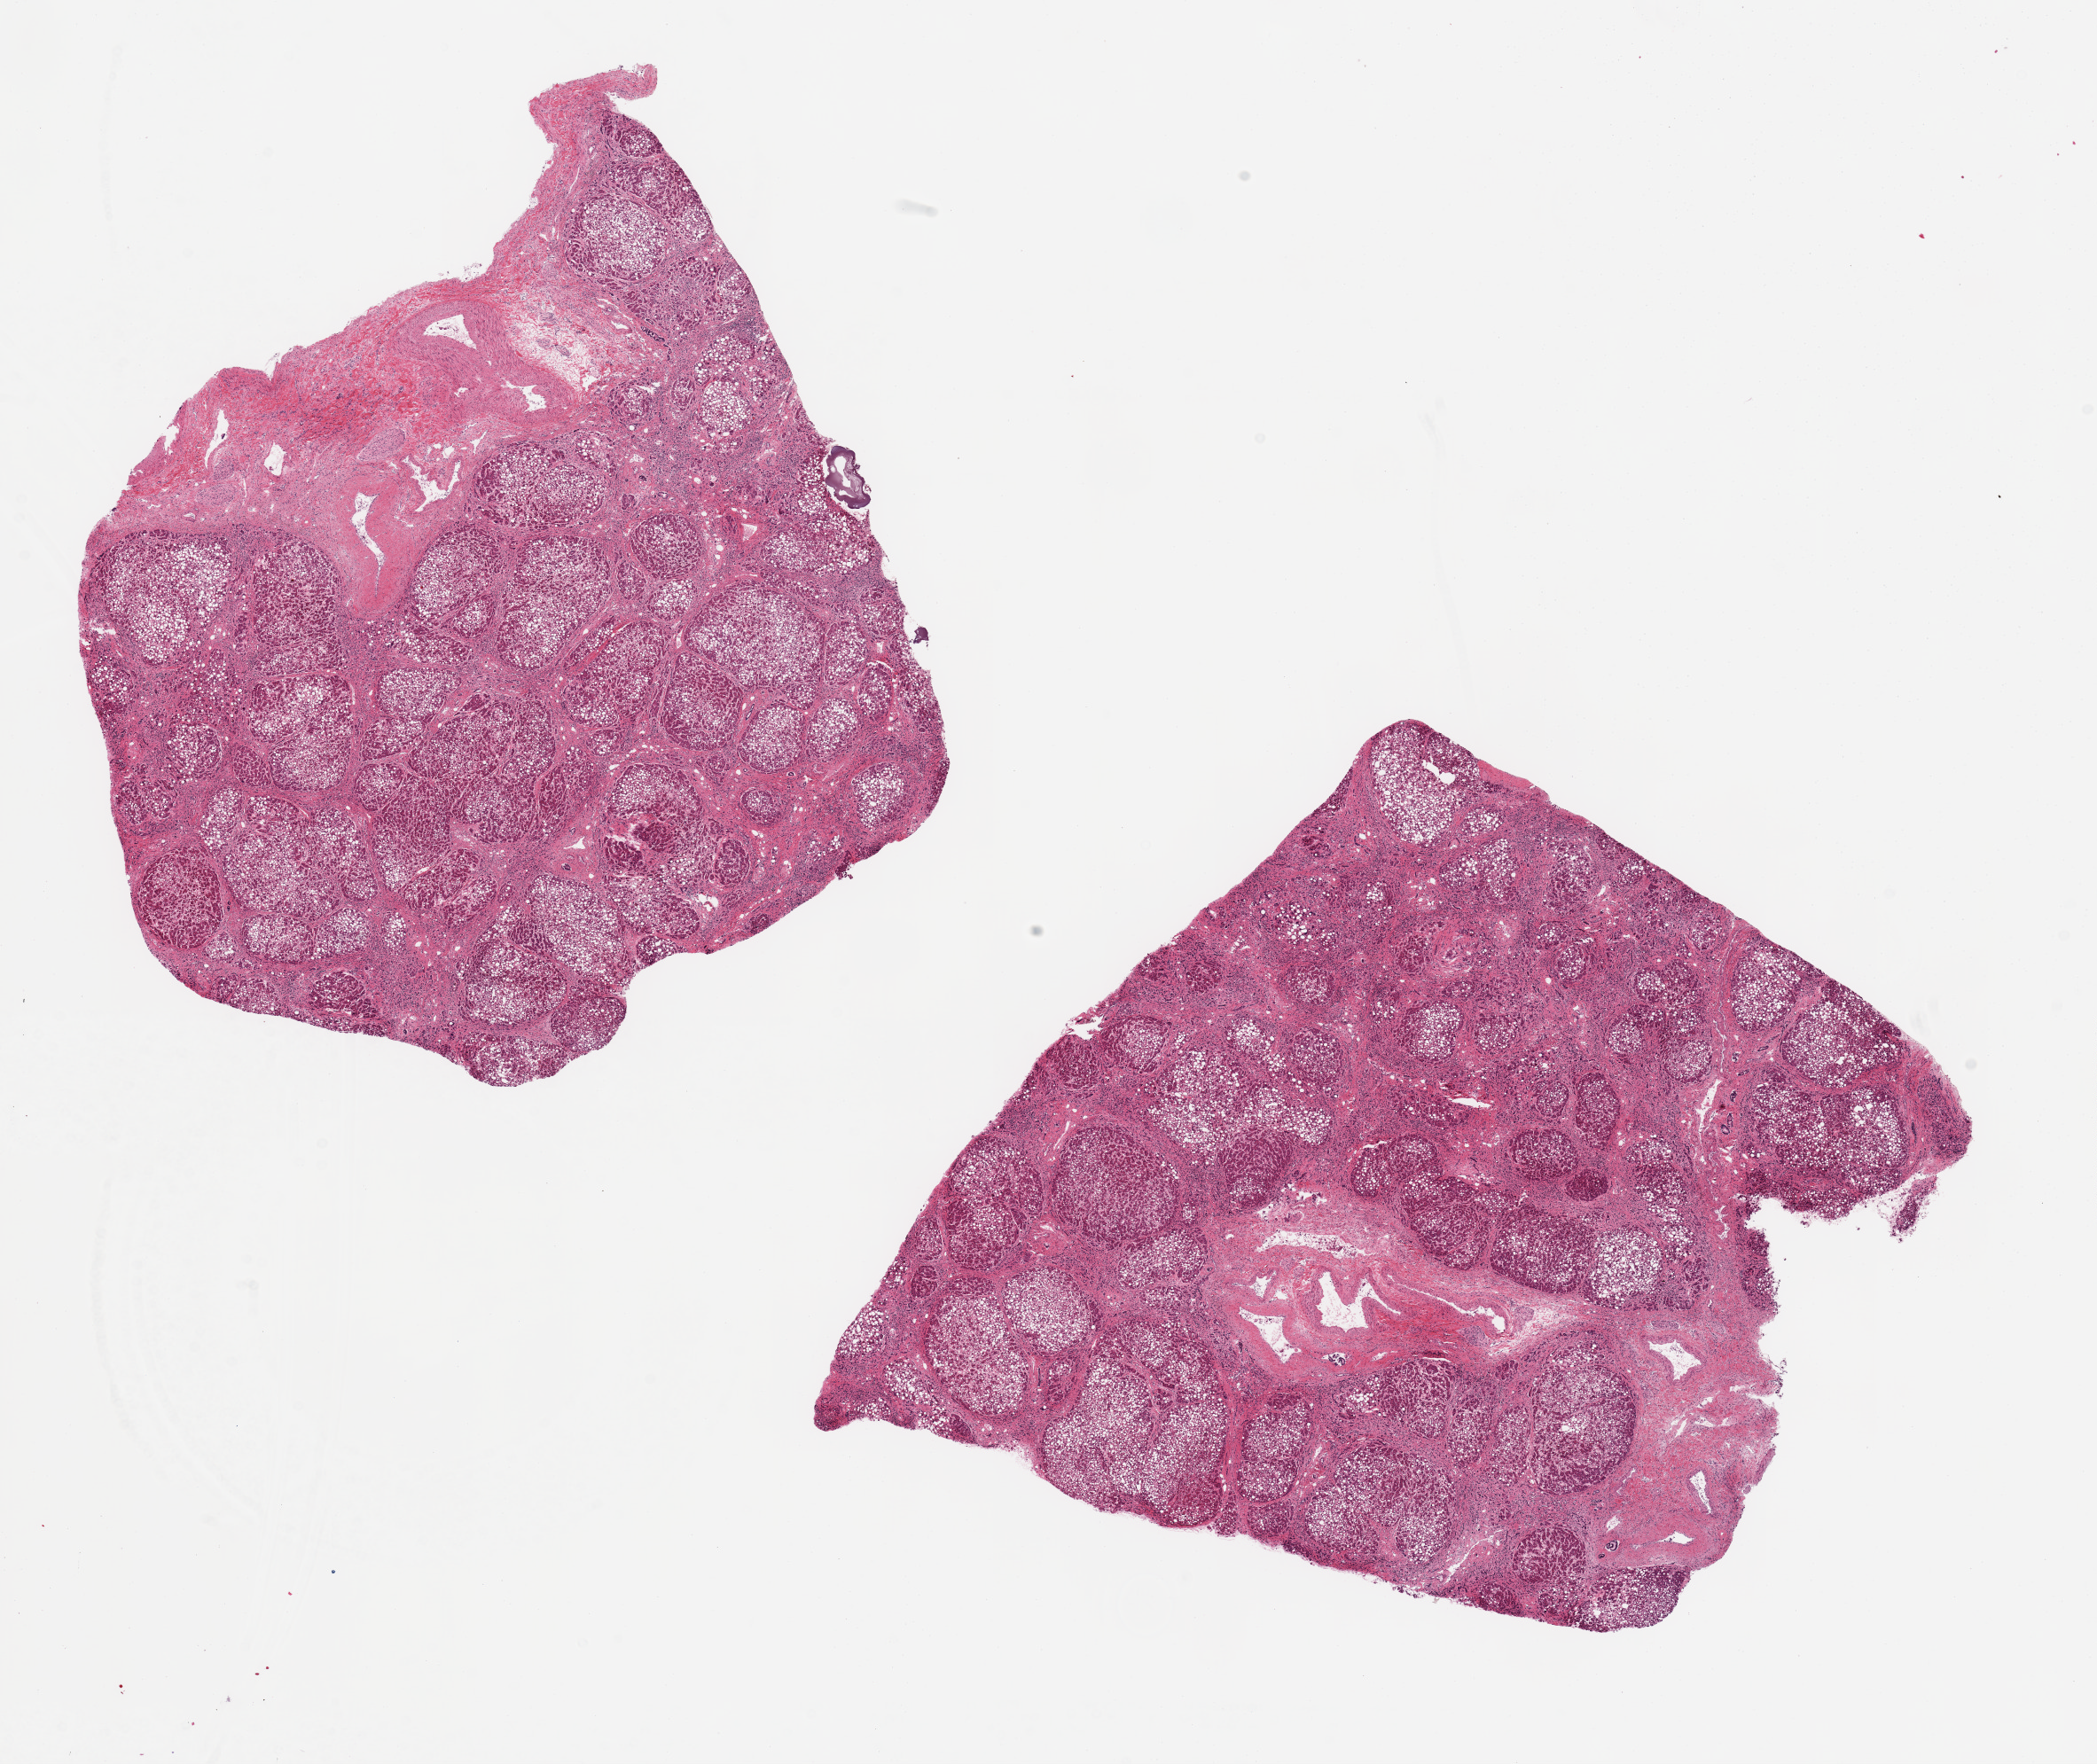
Digitized H&E-stained section, whole scanned area (about 18.7 x 15.7 mm) shown as a low-resolution overview. PAXgene-fixed, paraffin-embedded tissue. Section of liver (target tissue). Tissue donor sample. Male donor.
• review note (as recorded): 2 pieces ~7.5x7.5mm. Established micronodular cirrhosis with micro and macrovesicular steatosis and chronic hepatitis